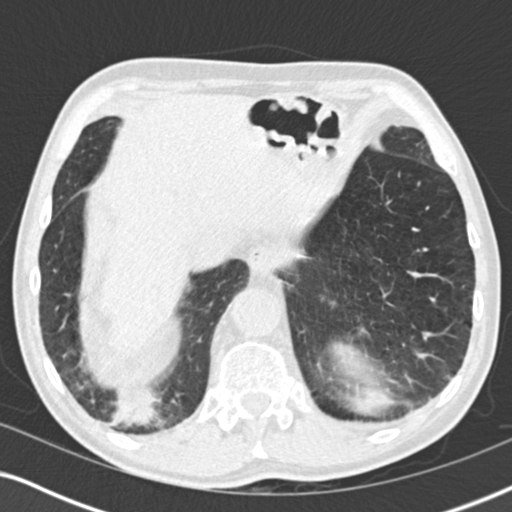
Chest CT (low-dose screening protocol), one axial image, baseline annual screen, lung window (W 1500 / L -600 HU), 2 mm slice thickness, 120 kVp. Male, age 64 years at enrolment. Former smoker at enrolment.
Lesion marked by an expert reader, bounding box <74,361,181,453> (left, top, right, bottom; pixels). The screening reader recorded 3 non-calcified nodules or masses ≥4 mm on this exam (lingula, lingula, right lower lobe); which of them this box marks is not recorded.